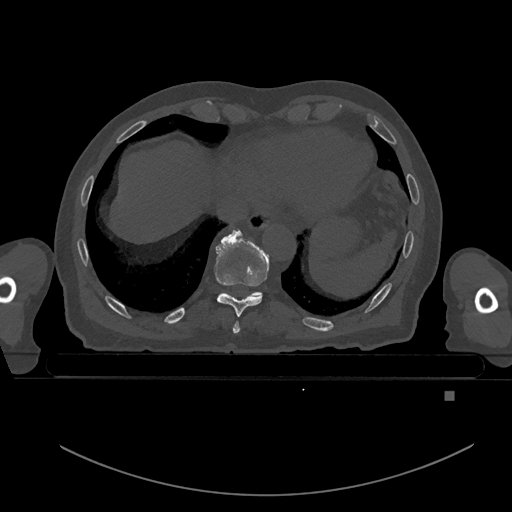
CT including the spine, one axial slice. Slice 137 of 969 in the series (ordered by position). Bone window (W 1800 / L 400 HU). 0.5 mm slice thickness. 512 × 512 image matrix. Male patient, age 82 years. From the clinical record (not read from this slice): primary cancer: prostate.
Annotated regions visible in this slice (semi-automatic segmentation, software-assisted and operator-edited):
- T10 vertebra: bounding box <254,291,261,295> (left, top, right, bottom; pixels)
- T8 vertebra: <233,321,240,334>
- T9 vertebra: <214,230,269,317>